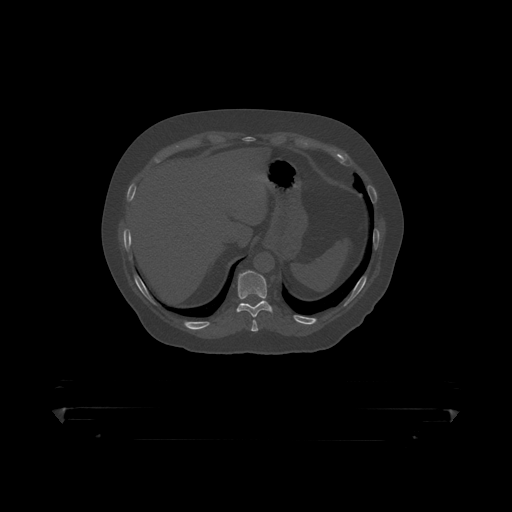
CT including the spine, one axial slice. Position 216 of 390 along the scan axis. Reconstruction kernel STANDARD. 120 kVp. Bone window (W 1800 / L 400 HU). 1.25 mm slice thickness. 512 × 512 image matrix, field of view 650 × 650 mm. Male patient, age 60 years. From the clinical record (not read from this slice): primary cancer: prostate.
Annotated regions visible in this slice (semi-automatically segmented with operator editing):
- T10 vertebra: bounding box <236,271,273,318> (left, top, right, bottom; pixels)